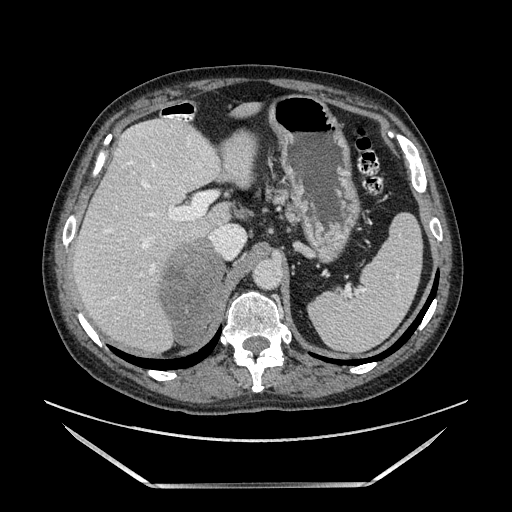
Contrast-enhanced abdominal CT, one axial slice; slice 101 of 185 in the series (ordered by position); soft-tissue window (W 400 / L 40 HU); 1.25 mm slice thickness; 512 × 512 image matrix. Male patient. Case-level facts recorded for this patient, not image findings: diagnosis: adrenocortical carcinoma; tumour side: right adrenal.
Outlined on this slice (semi-automatic segmentation, software-assisted and operator-edited):
- mass: bounding box (x1, y1, x2, y2) in pixels: (155, 234, 226, 342)